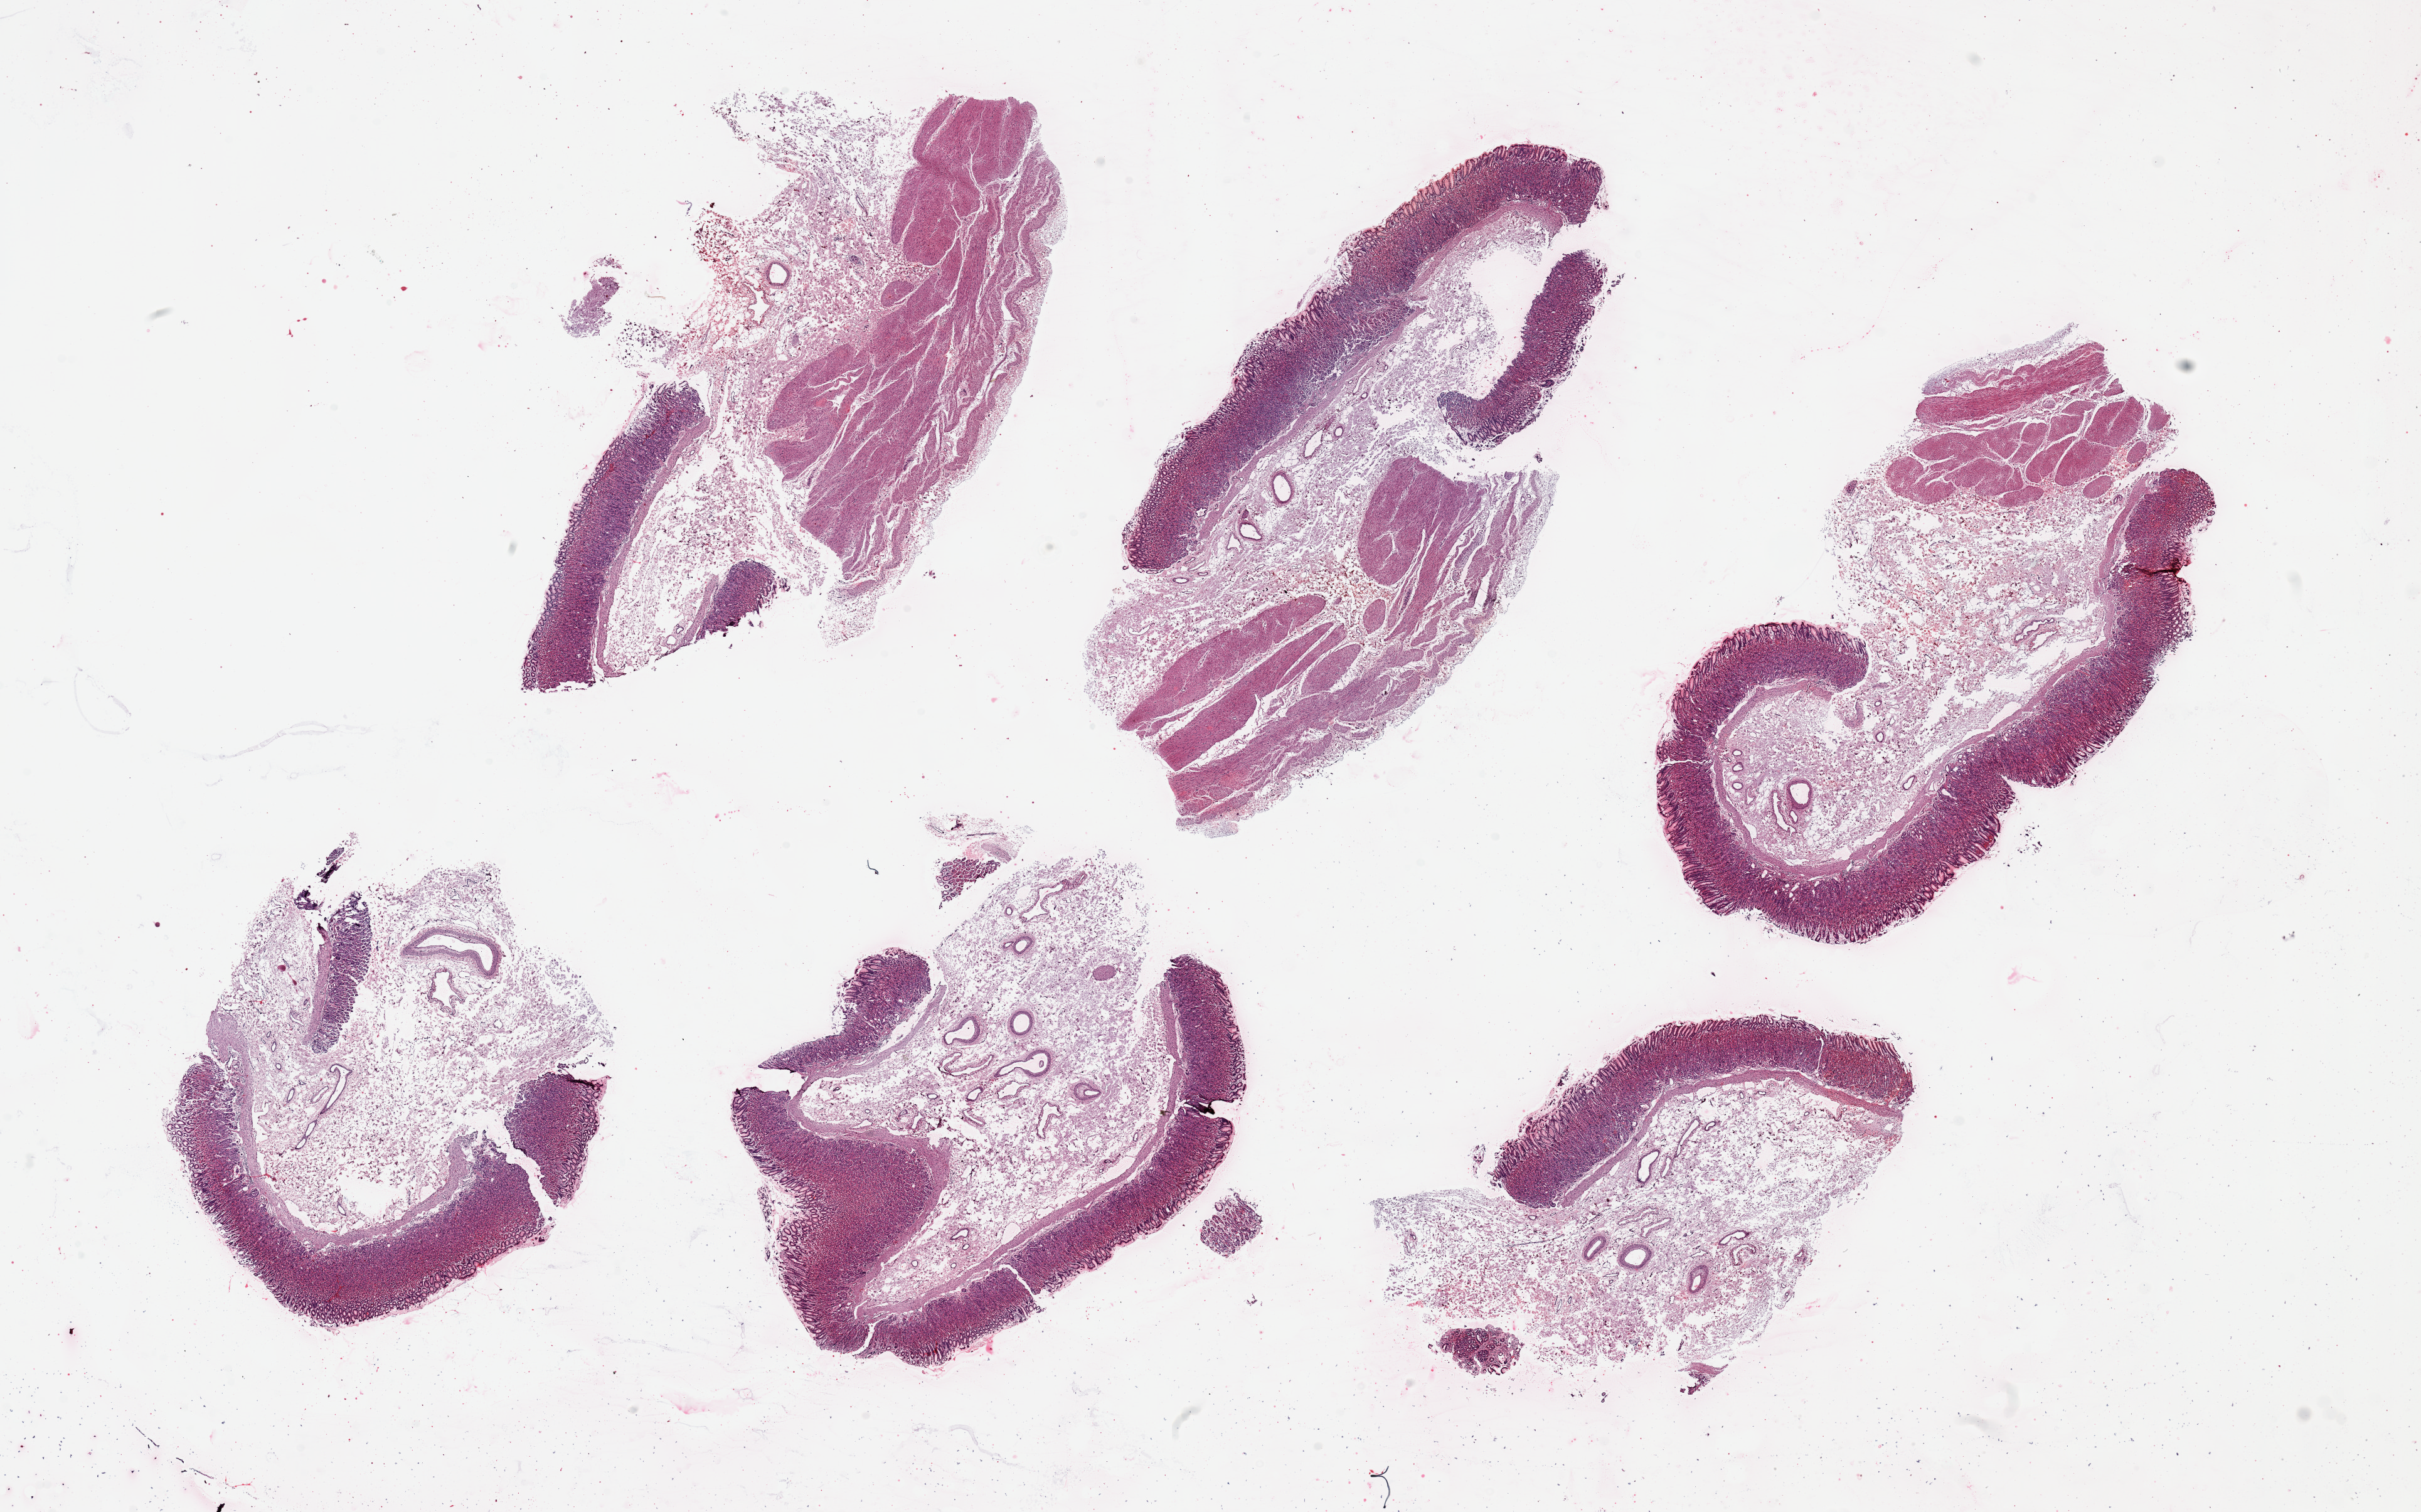
Digitized haematoxylin and eosin-stained section — whole scanned area (about 30.5 x 19.1 mm, slide scanned at 20x) shown as a low-resolution overview, PAXgene-fixed, paraffin-embedded tissue, target tissue: stomach, donor tissue sample.
Reviewer comment on this tissue sample: 6 pieces up to 10x4 mm; 3 with muscularis; all with mucosa.